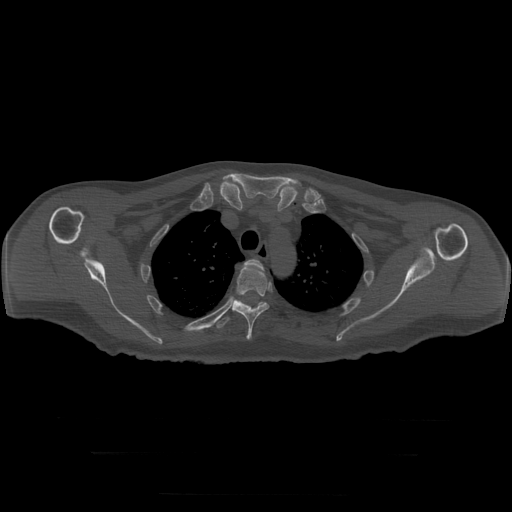
CT including the spine, one axial slice; position 240 of 397 along the scan axis; 120 kVp; bone window (W 1800 / L 400 HU); 1.25 mm slice thickness; 512 × 512 image matrix, field of view 510 × 510 mm. Patient age 73 years. Case-level facts recorded for this patient, not image findings: primary cancer: prostate.
Annotated regions visible in this slice (semi-automatic segmentation, software-assisted and operator-edited):
- T3 vertebra: bounding box <245,260,264,271> (left, top, right, bottom; pixels)
- T4 vertebra: <233,266,270,340>
- T5 vertebra: <217,298,263,329>